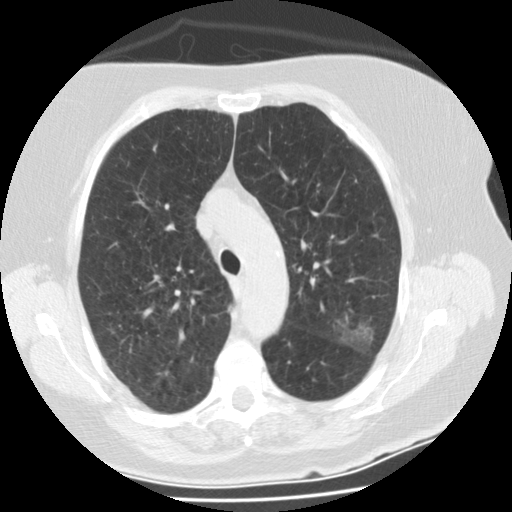
Chest CT (low-dose screening protocol), one axial image; second screening round (one year after baseline); lung window (W 1500 / L -600 HU); 512 × 512 image matrix, field of view 321 × 321 mm. Female participant, aged 74 years at enrolment.
Lesion marked by an expert reader, bounding box (x1, y1, x2, y2) in pixels: (327, 308, 386, 360). The screening reader recorded 3 non-calcified nodules or masses ≥4 mm on this exam (right lower lobe, left upper lobe, left upper lobe); which of them this box marks is not recorded. Lung cancer was diagnosed 68 days after this screen: bronchiolo-alveolar adenocarcinoma, NOS, left upper lobe, stage IA (AJCC 6th edition), 20 mm at pathology.